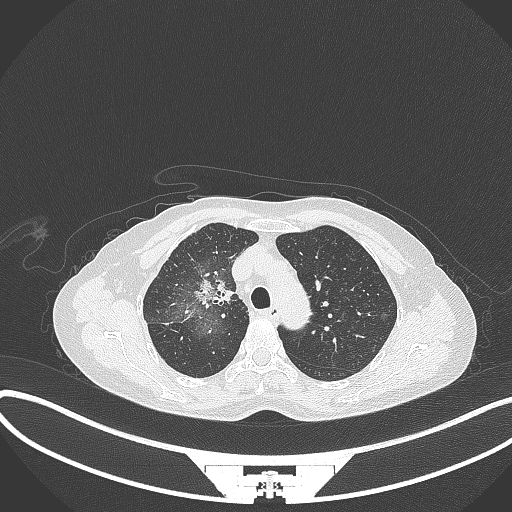
Chest CT, one axial slice; position 232 of 284 along the scan axis; reconstruction kernel B70f; 120 kVp; lung window (W 1500 / L -600 HU); 512 × 512 image matrix, field of view 400 × 400 mm. Patient: female, 59 years. Case-level facts recorded for this patient, not image findings: clinical TNM (as recorded): T3 N0 M0; histopathological grade: G1.
Outlined on this slice (rectangle marked by the reading radiologist):
- lung tumour (recorded histology: adenocarcinoma): bounding box [x1, y1, x2, y2] px = [194, 272, 233, 308]